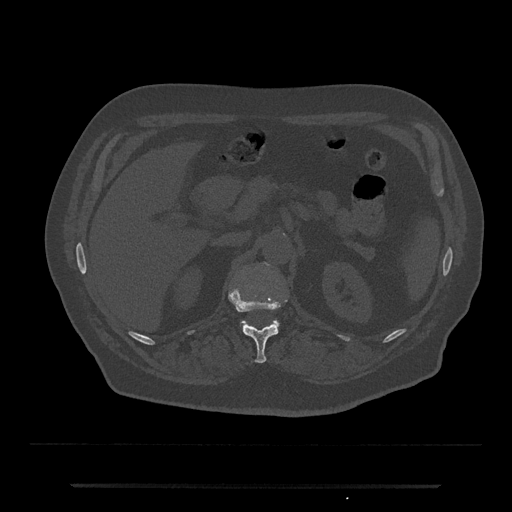
CT including the spine, one axial slice. Position 577 of 797 along the scan axis. Bone window (W 1800 / L 400 HU). 0.5 mm slice thickness. 512 × 512 image matrix, field of view 434 × 434 mm. Male patient, age 80 years. From the clinical record (not read from this slice): primary cancer: prostate.
Outlined on this slice (semi-automatically segmented with operator editing):
- L1 vertebra: bounding box <240,263,280,328> (left, top, right, bottom; pixels)
- T12 vertebra: <229,290,279,363>